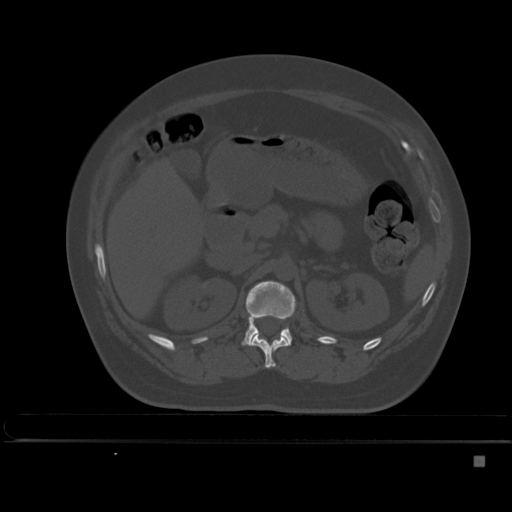
CT including the spine, one axial slice. Slice 203 of 495 in the series (ordered by position). Bone window (W 1800 / L 400 HU). 1.5 mm slice thickness. 512 × 512 image matrix, field of view 404 × 404 mm. Patient: female, 33 years. From the clinical record (not read from this slice): primary cancer: breast.
Outlined on this slice (semi-automatic segmentation, software-assisted and operator-edited):
- L1 vertebra: bounding box <242,280,296,346> (left, top, right, bottom; pixels)
- T12 vertebra: <249,333,289,368>